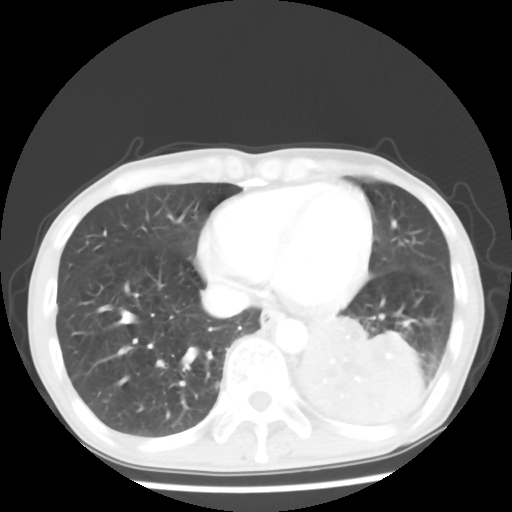
Chest CT, one axial slice; position 19 of 64 along the scan axis; reconstruction kernel STANDARD; 120 kVp; lung window (W 1500 / L -600 HU); 512 × 512 image matrix, field of view 313 × 313 mm. Male patient, age 68 years. Case-level facts recorded for this patient, not image findings: clinical TNM (as recorded): T4 N0 M0.
Annotated regions visible in this slice (rectangle marked by the reading radiologist):
- lung tumour (recorded histology: squamous cell carcinoma): box from (x=285, y=307) to (x=426, y=436) px